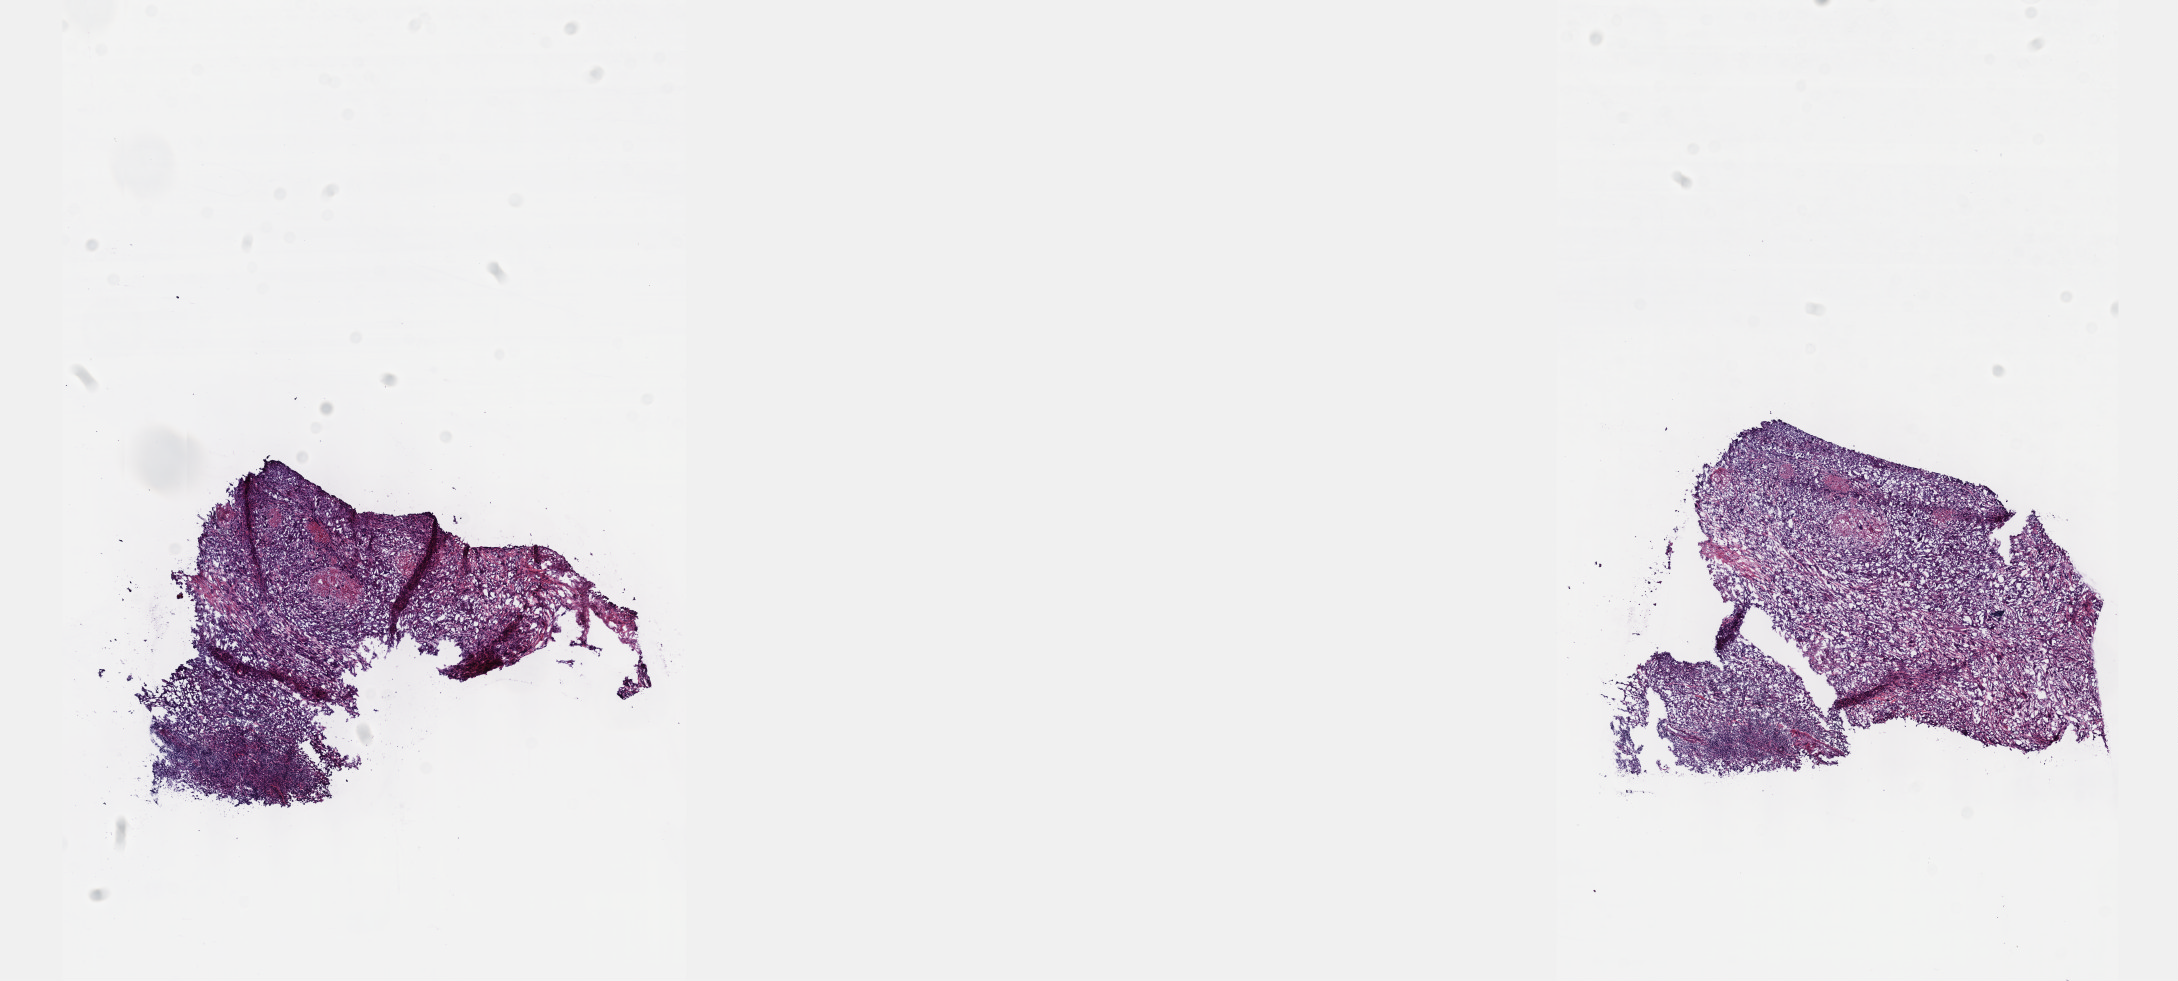
H&E-stained whole-slide image — low-resolution overview of the scanned area, about 17.6 x 7.9 mm; frozen section from the top of the tissue portion; bladder, primary tumour sample. Patient: female, age at initial diagnosis 60 years.
Histologic diagnosis: Transitional cell carcinoma.